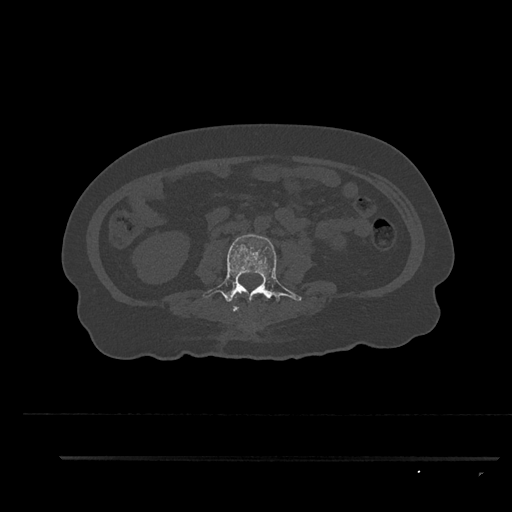
CT including the spine, one axial slice. Bone window (W 1800 / L 400 HU). 0.5 mm slice thickness. 512 × 512 image matrix, field of view 408 × 408 mm. Patient: female, 44 years. From the clinical record (not read from this slice): primary cancer: renal; vertebrae with lytic lesions (as recorded): L1.
Annotated regions visible in this slice (semi-automatic segmentation, software-assisted and operator-edited):
- L2 vertebra: bounding box [x1, y1, x2, y2] px = [232, 295, 240, 311]
- L3 vertebra: [203, 234, 302, 312]